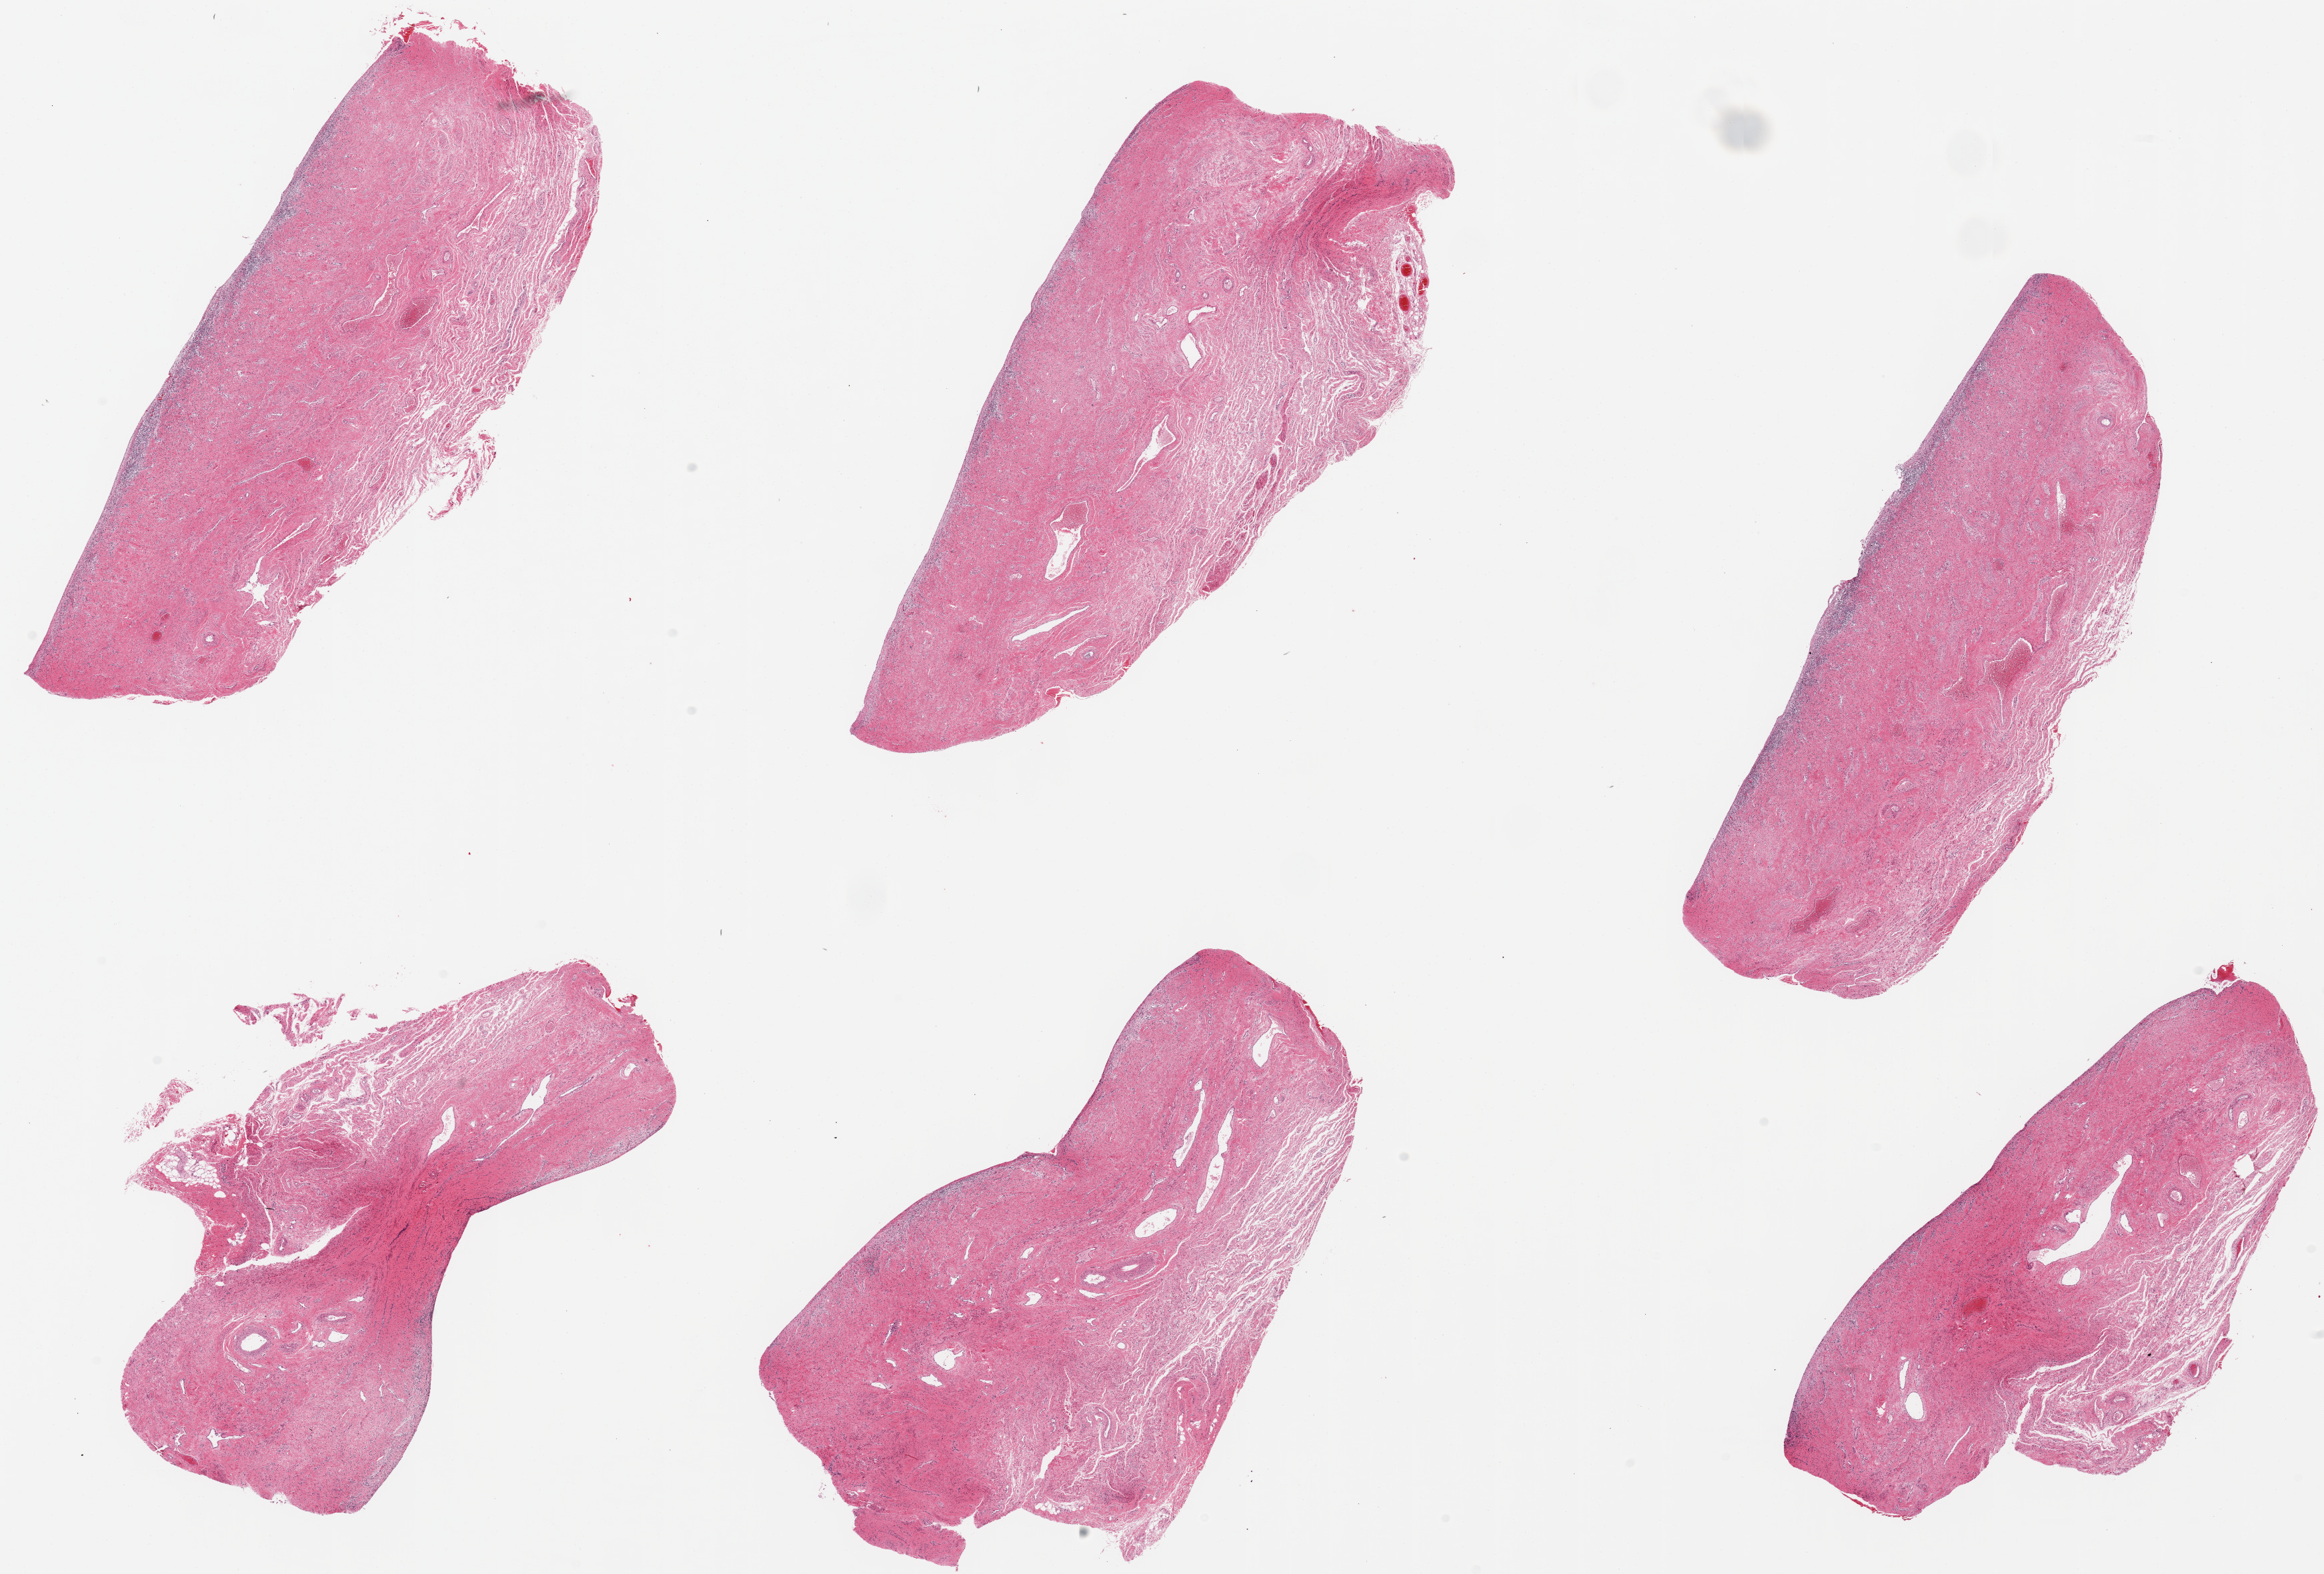
Whole-slide image, H&E stain, brightfield — low-resolution overview of the scanned area, about 27.6 x 18.7 mm; PAXgene-fixed paraffin-embedded (PFPE) section; target tissue: vagina; donor tissue sample. Donor sex: female.
- pathologist's review note for this sample: 6 pieces. up to 8x2mm; Specimens represent only fibromuscular wall; epithelium is absent, sloughed? Chronic inflammation